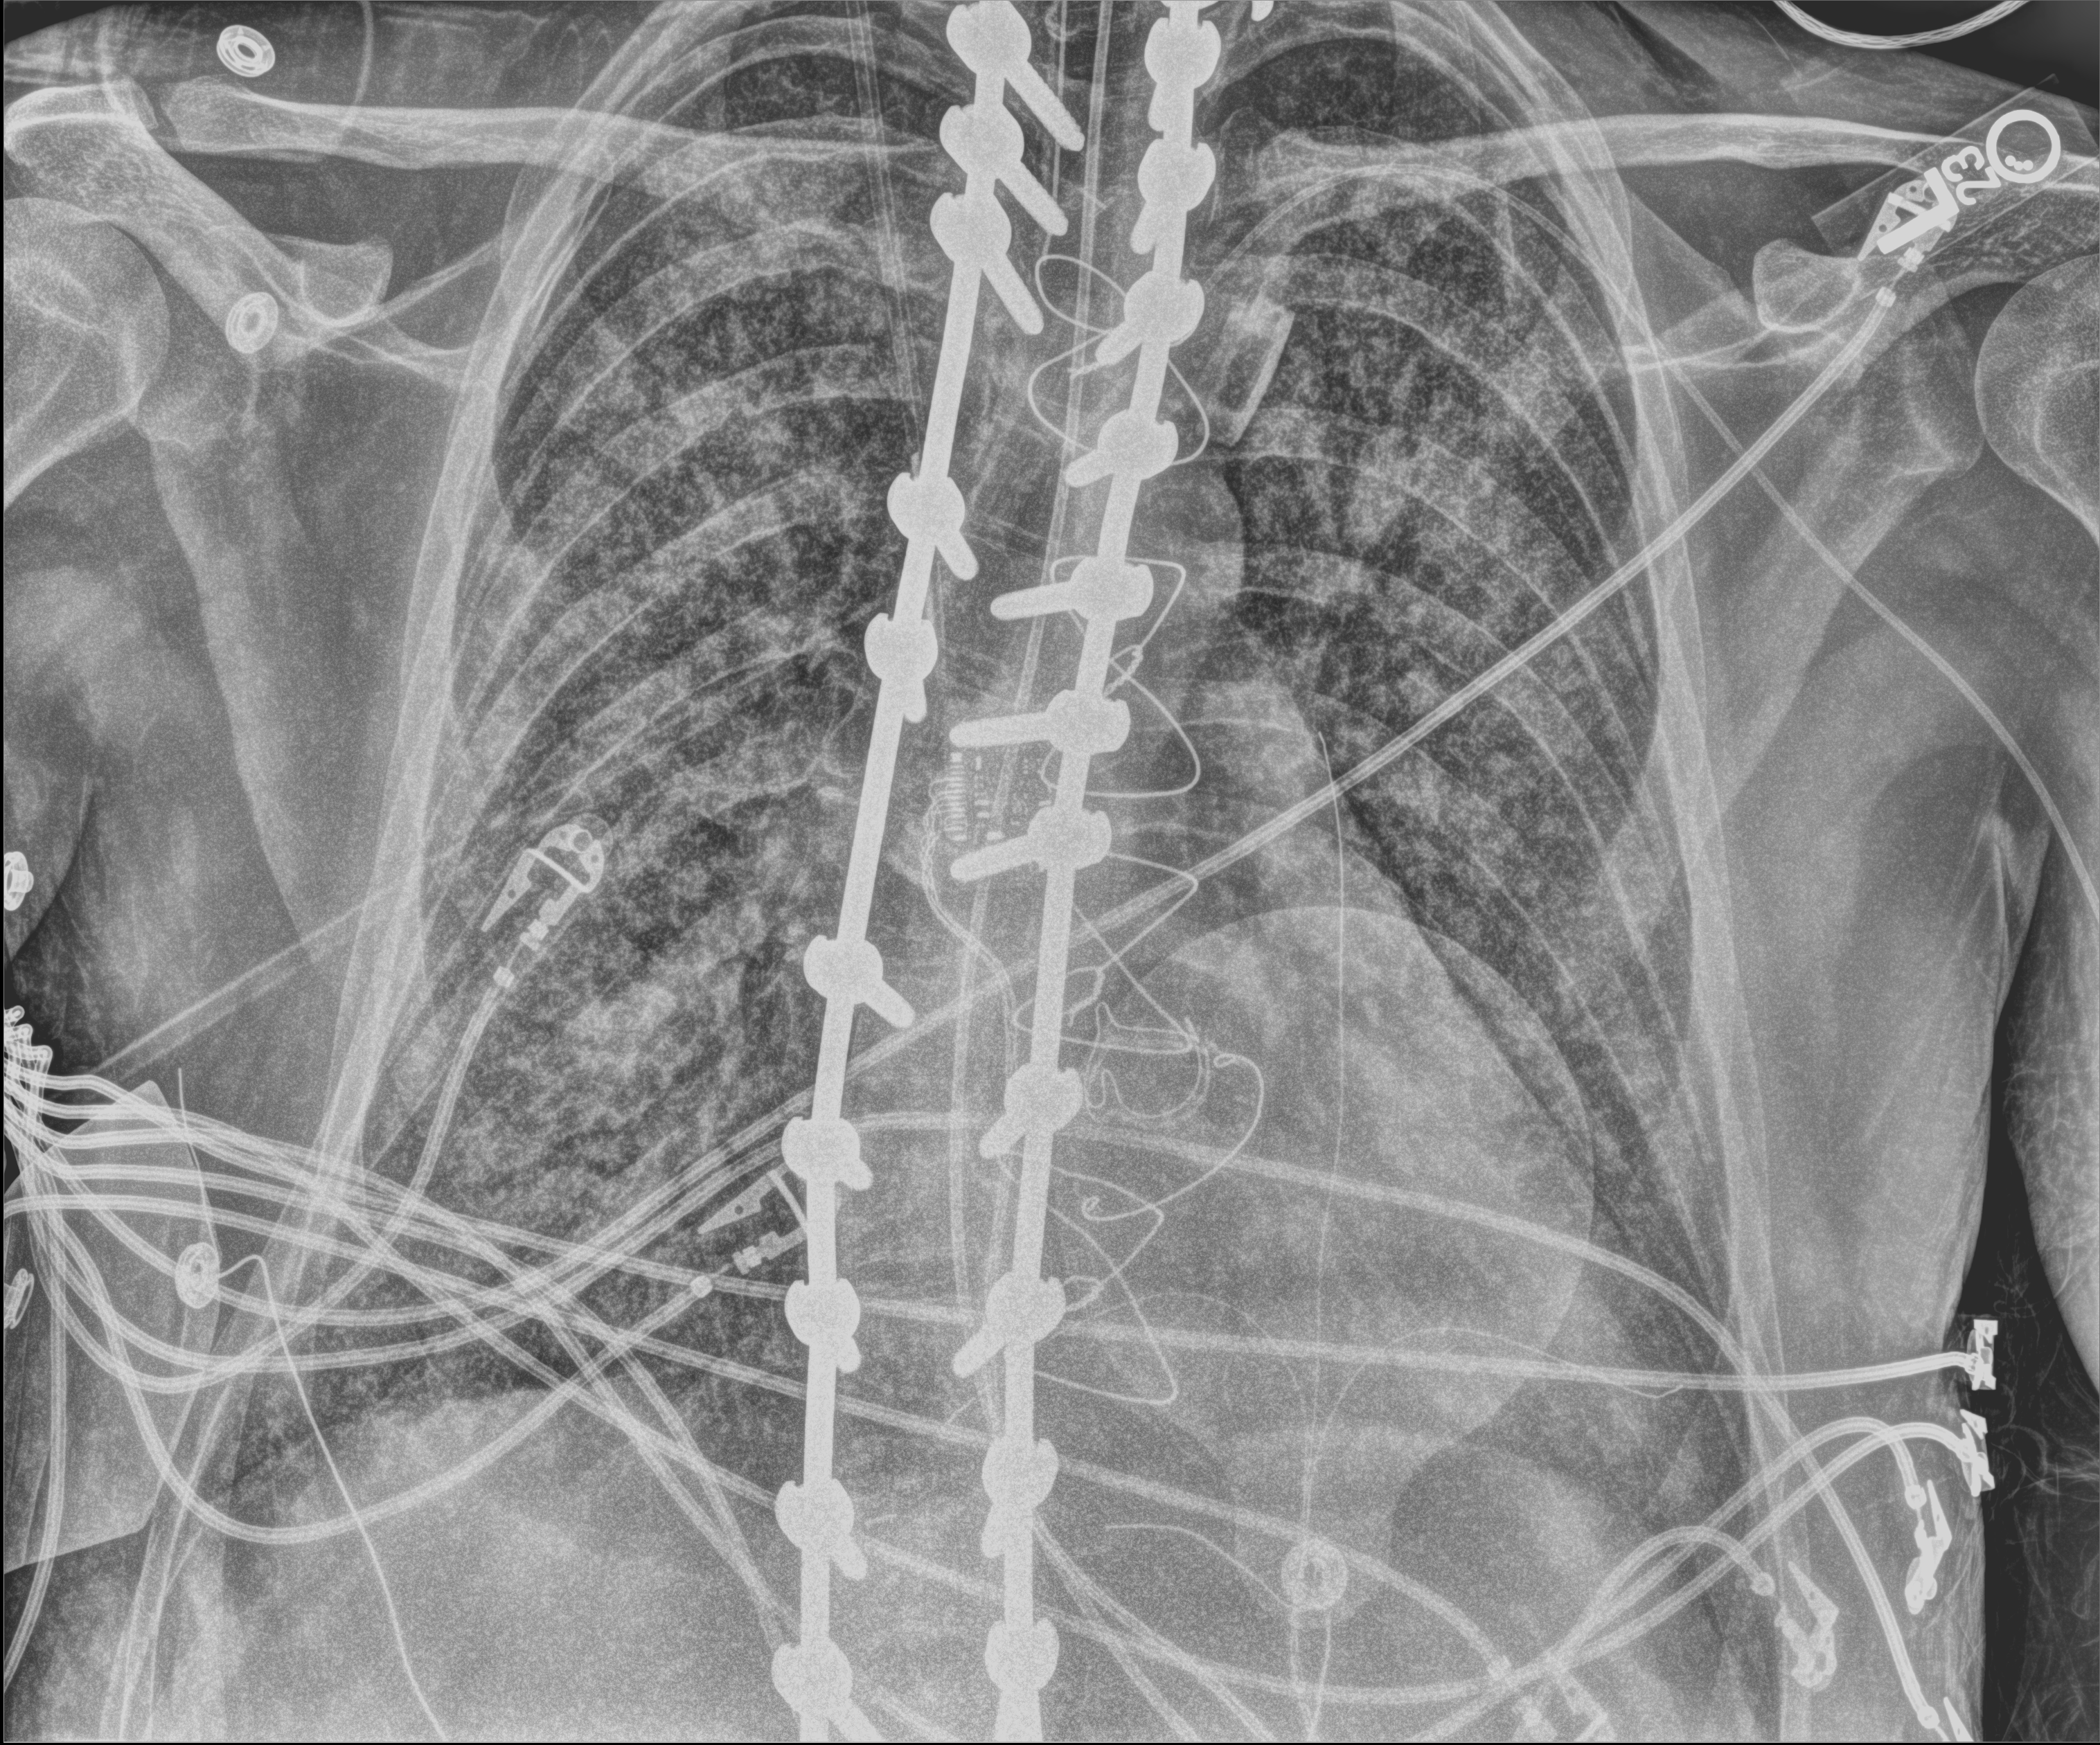
Chest X-ray (portable). Patient hospitalised with COVID-19, aged 18–59 years.
Hospital-stay facts (about this admission, not read from this image; timing relative to this image not recorded): COPD (admission record): no; admitted to intensive care during this hospital stay: yes; mechanically ventilated during this hospital stay: yes.